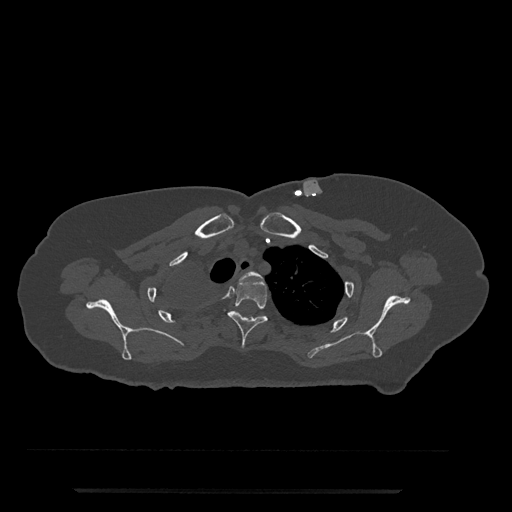
CT including the spine, one axial slice; position 631 of 797 along the scan axis; reconstruction kernel Br40s/3; bone window (W 1800 / L 400 HU); 0.5 mm slice thickness; 512 × 512 image matrix. Patient: female, 51 years. From the clinical record (not read from this slice): primary cancer: neuro.
Outlined on this slice (semi-automatic segmentation, software-assisted and operator-edited):
- T2 vertebra: bounding box <240,271,262,281> (left, top, right, bottom; pixels)
- T3 vertebra: <227,277,268,349>
- T4 vertebra: <233,310,264,318>